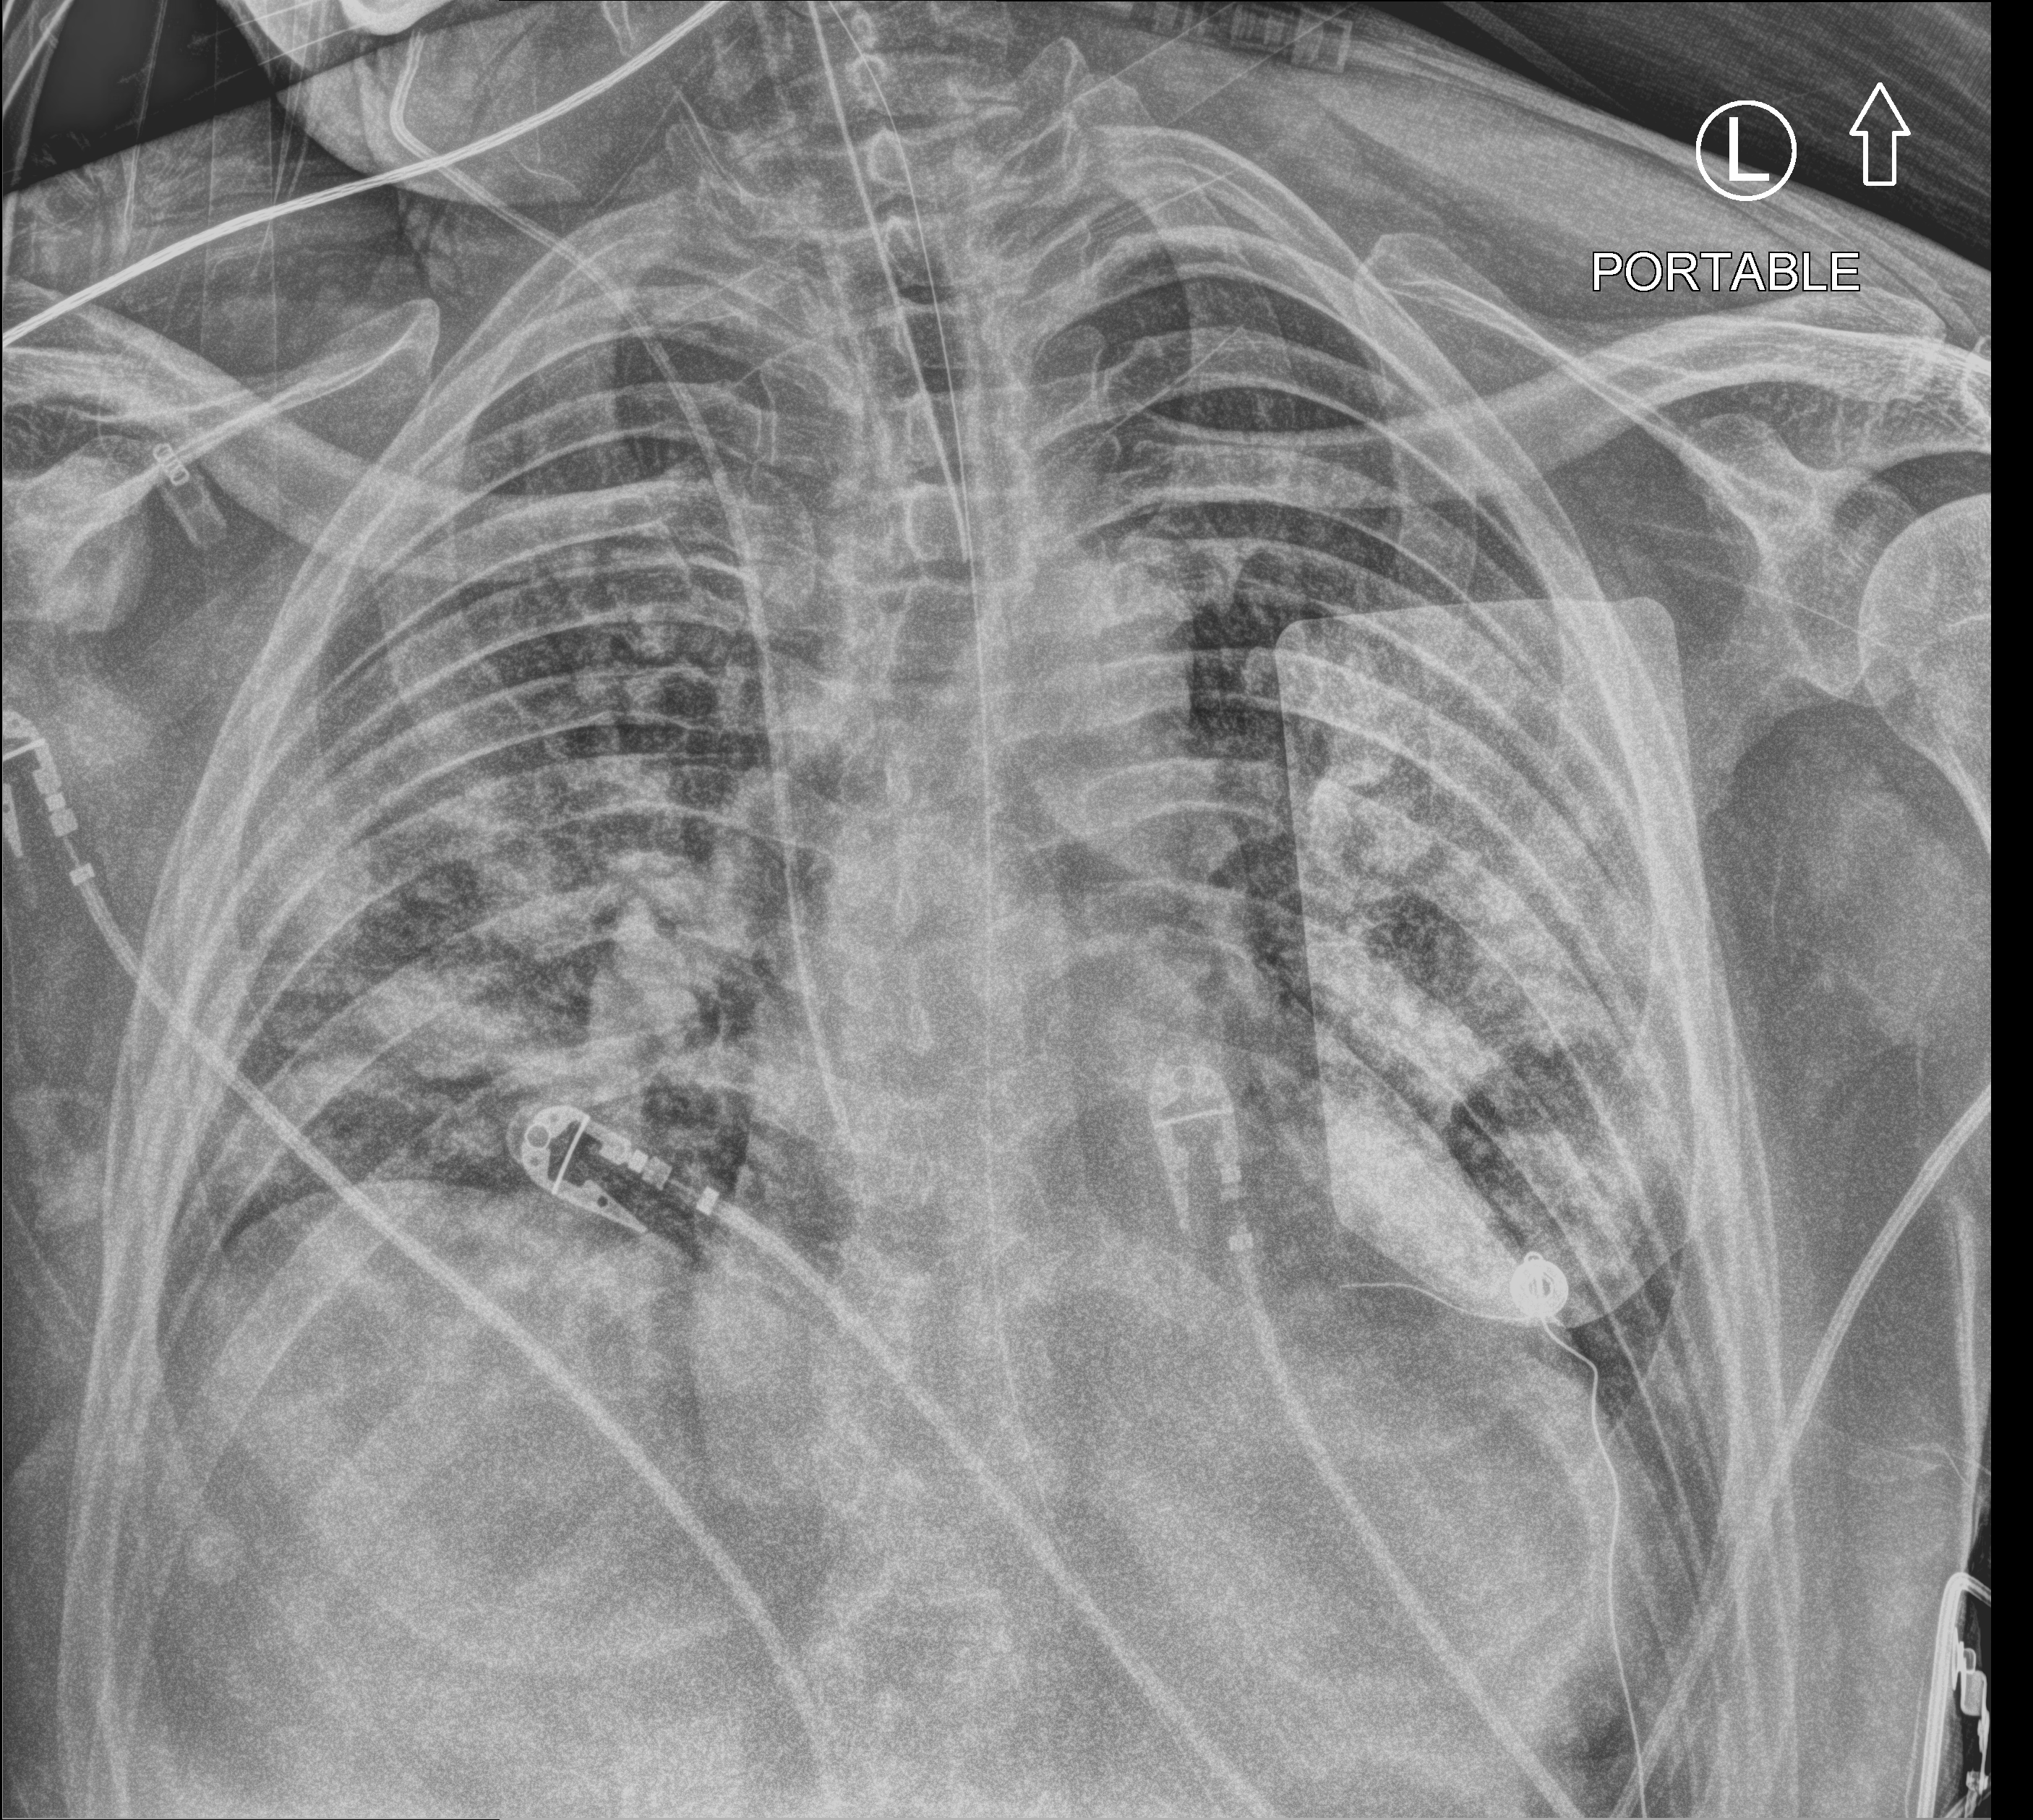
Chest X-ray (portable), anteroposterior (AP) projection. Patient hospitalised with COVID-19; male, aged 18–59 years.
From the hospital-stay record, not from the radiograph (when in the stay this image was taken is not recorded):
- chronic kidney disease (admission record): no
- length of hospital stay: 75 days
- admitted to intensive care during this hospital stay: yes